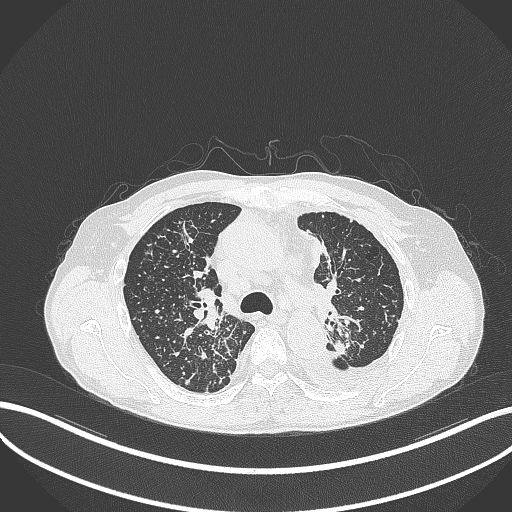
Chest CT, one axial slice. Slice 246 of 325 in the series (ordered by position). 120 kVp. Lung window (W 1500 / L -600 HU). 512 × 512 image matrix. Male patient, age 58 years. From the clinical record (not read from this slice): clinical TNM (as recorded): T1c N3 M1.
Outlined on this slice (bounding box drawn by a radiologist):
- lung tumour (recorded histology: adenocarcinoma): box from (x=332, y=333) to (x=348, y=358) px